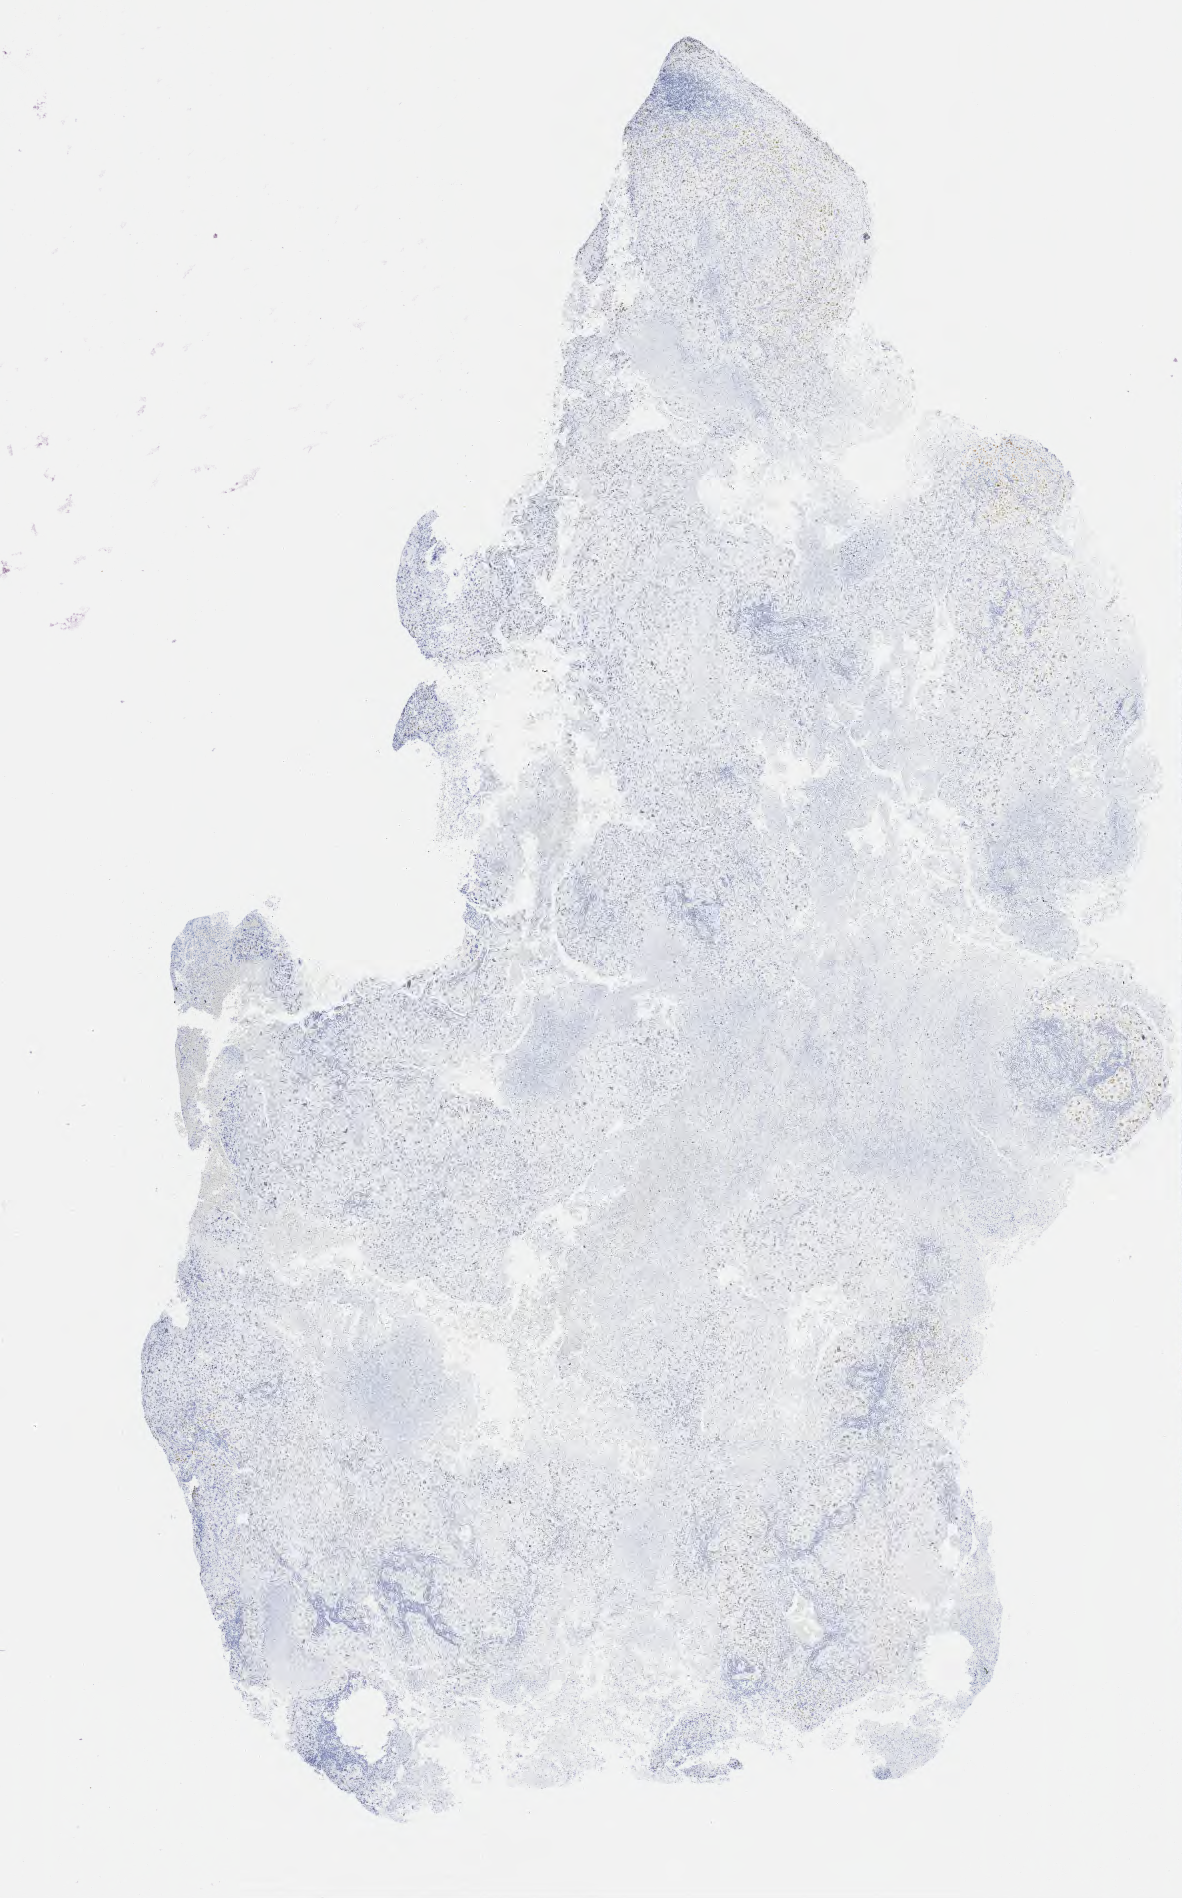
Whole-slide image, immunohistochemical stain for p40, low-resolution overview of the scanned area, about 9.6 x 15.4 mm. Patient sex: female.
Specimen: tumor tissue; site: lower respiratory tract.